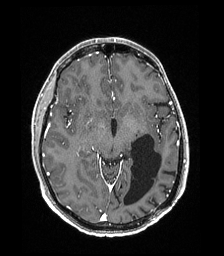
Brain MRI from a brain-tumour surgery series, one axial slice. Slice 103 of 192 in the series (ordered by position). T1-weighted post-contrast. 1 mm slice thickness. 224 × 256 image matrix, field of view 224 × 256 mm. Case-level facts recorded for this patient, not image findings: histopathology: Low grade glioma; IDH mutation: no; tumour location: Left Parieto-Occipital Intraventricular.
Structures marked on this image (expert manual segmentation):
- previous resection cavity: bounding box (x1, y1, x2, y2) in pixels: (124, 134, 162, 205)